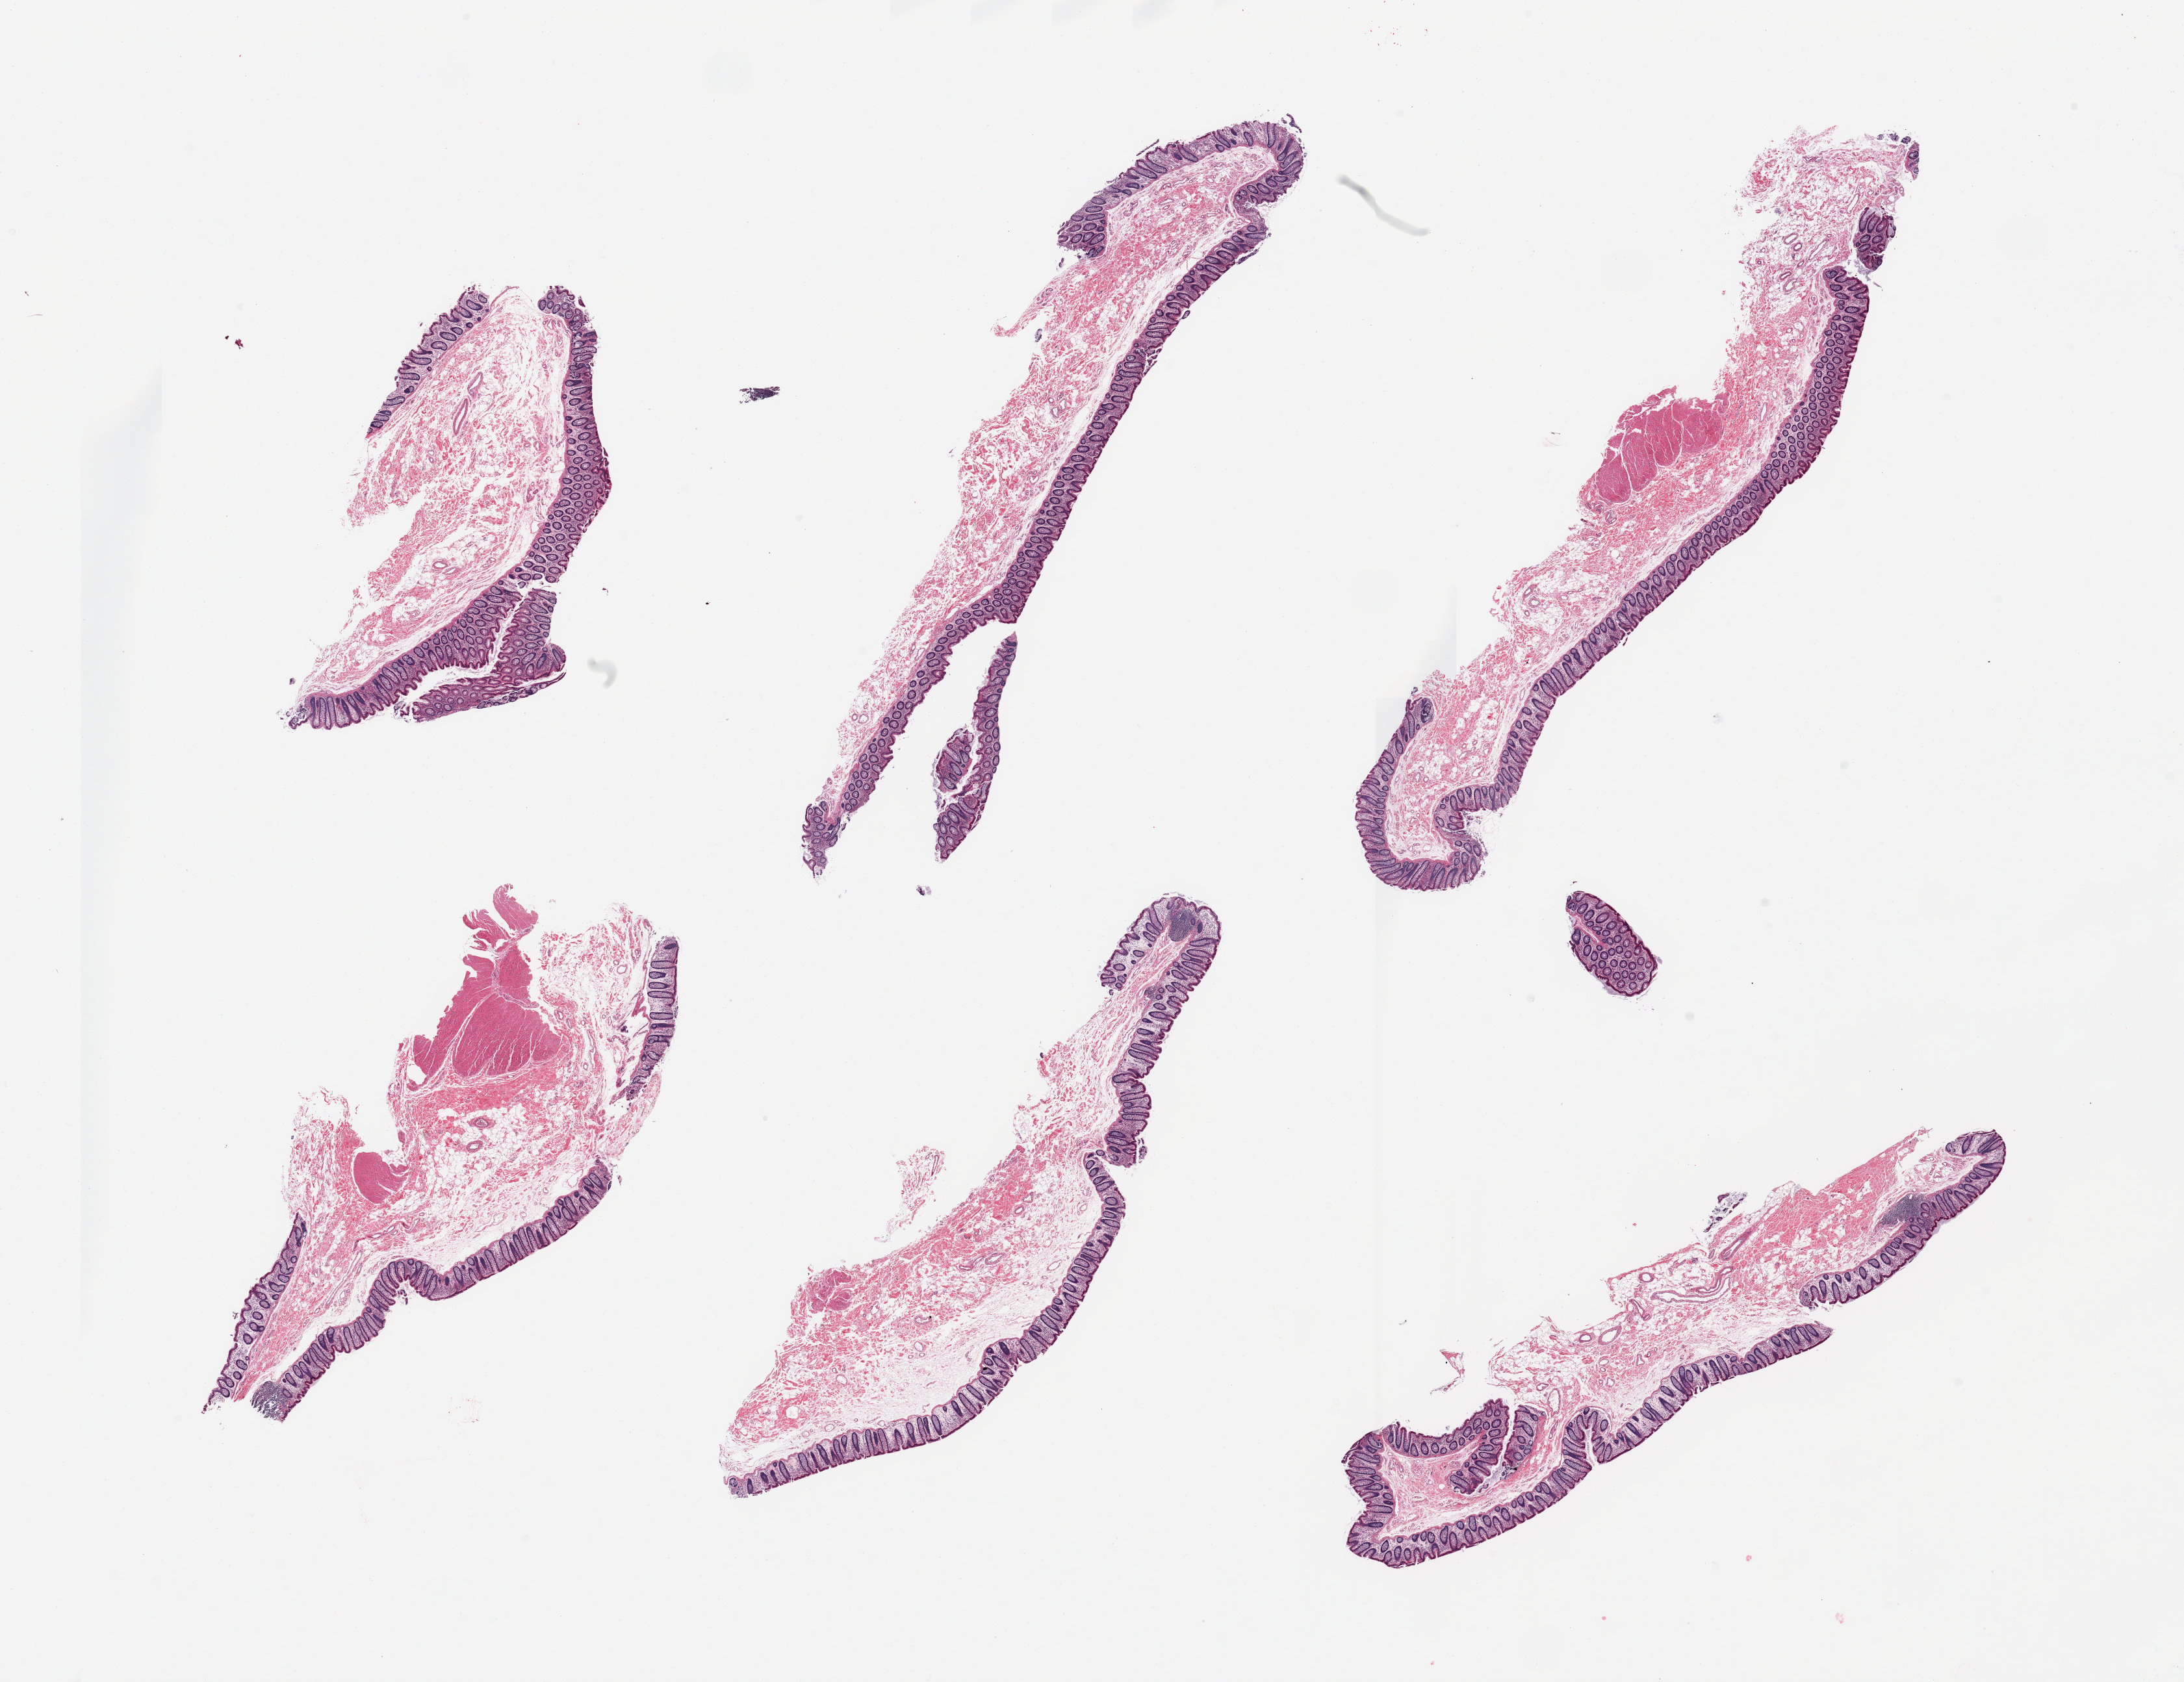
H&E whole-slide image — a low-resolution overview of the entire scanned area, about 26.6 x 20.5 mm. PAXgene-fixed, paraffin-embedded tissue. Target tissue: transverse colon. Tissue donor sample. Donor sex: male.
Reviewer comment on this tissue sample: 6 pieces; 4 have no muscle, 2 have small amounts of muscle.